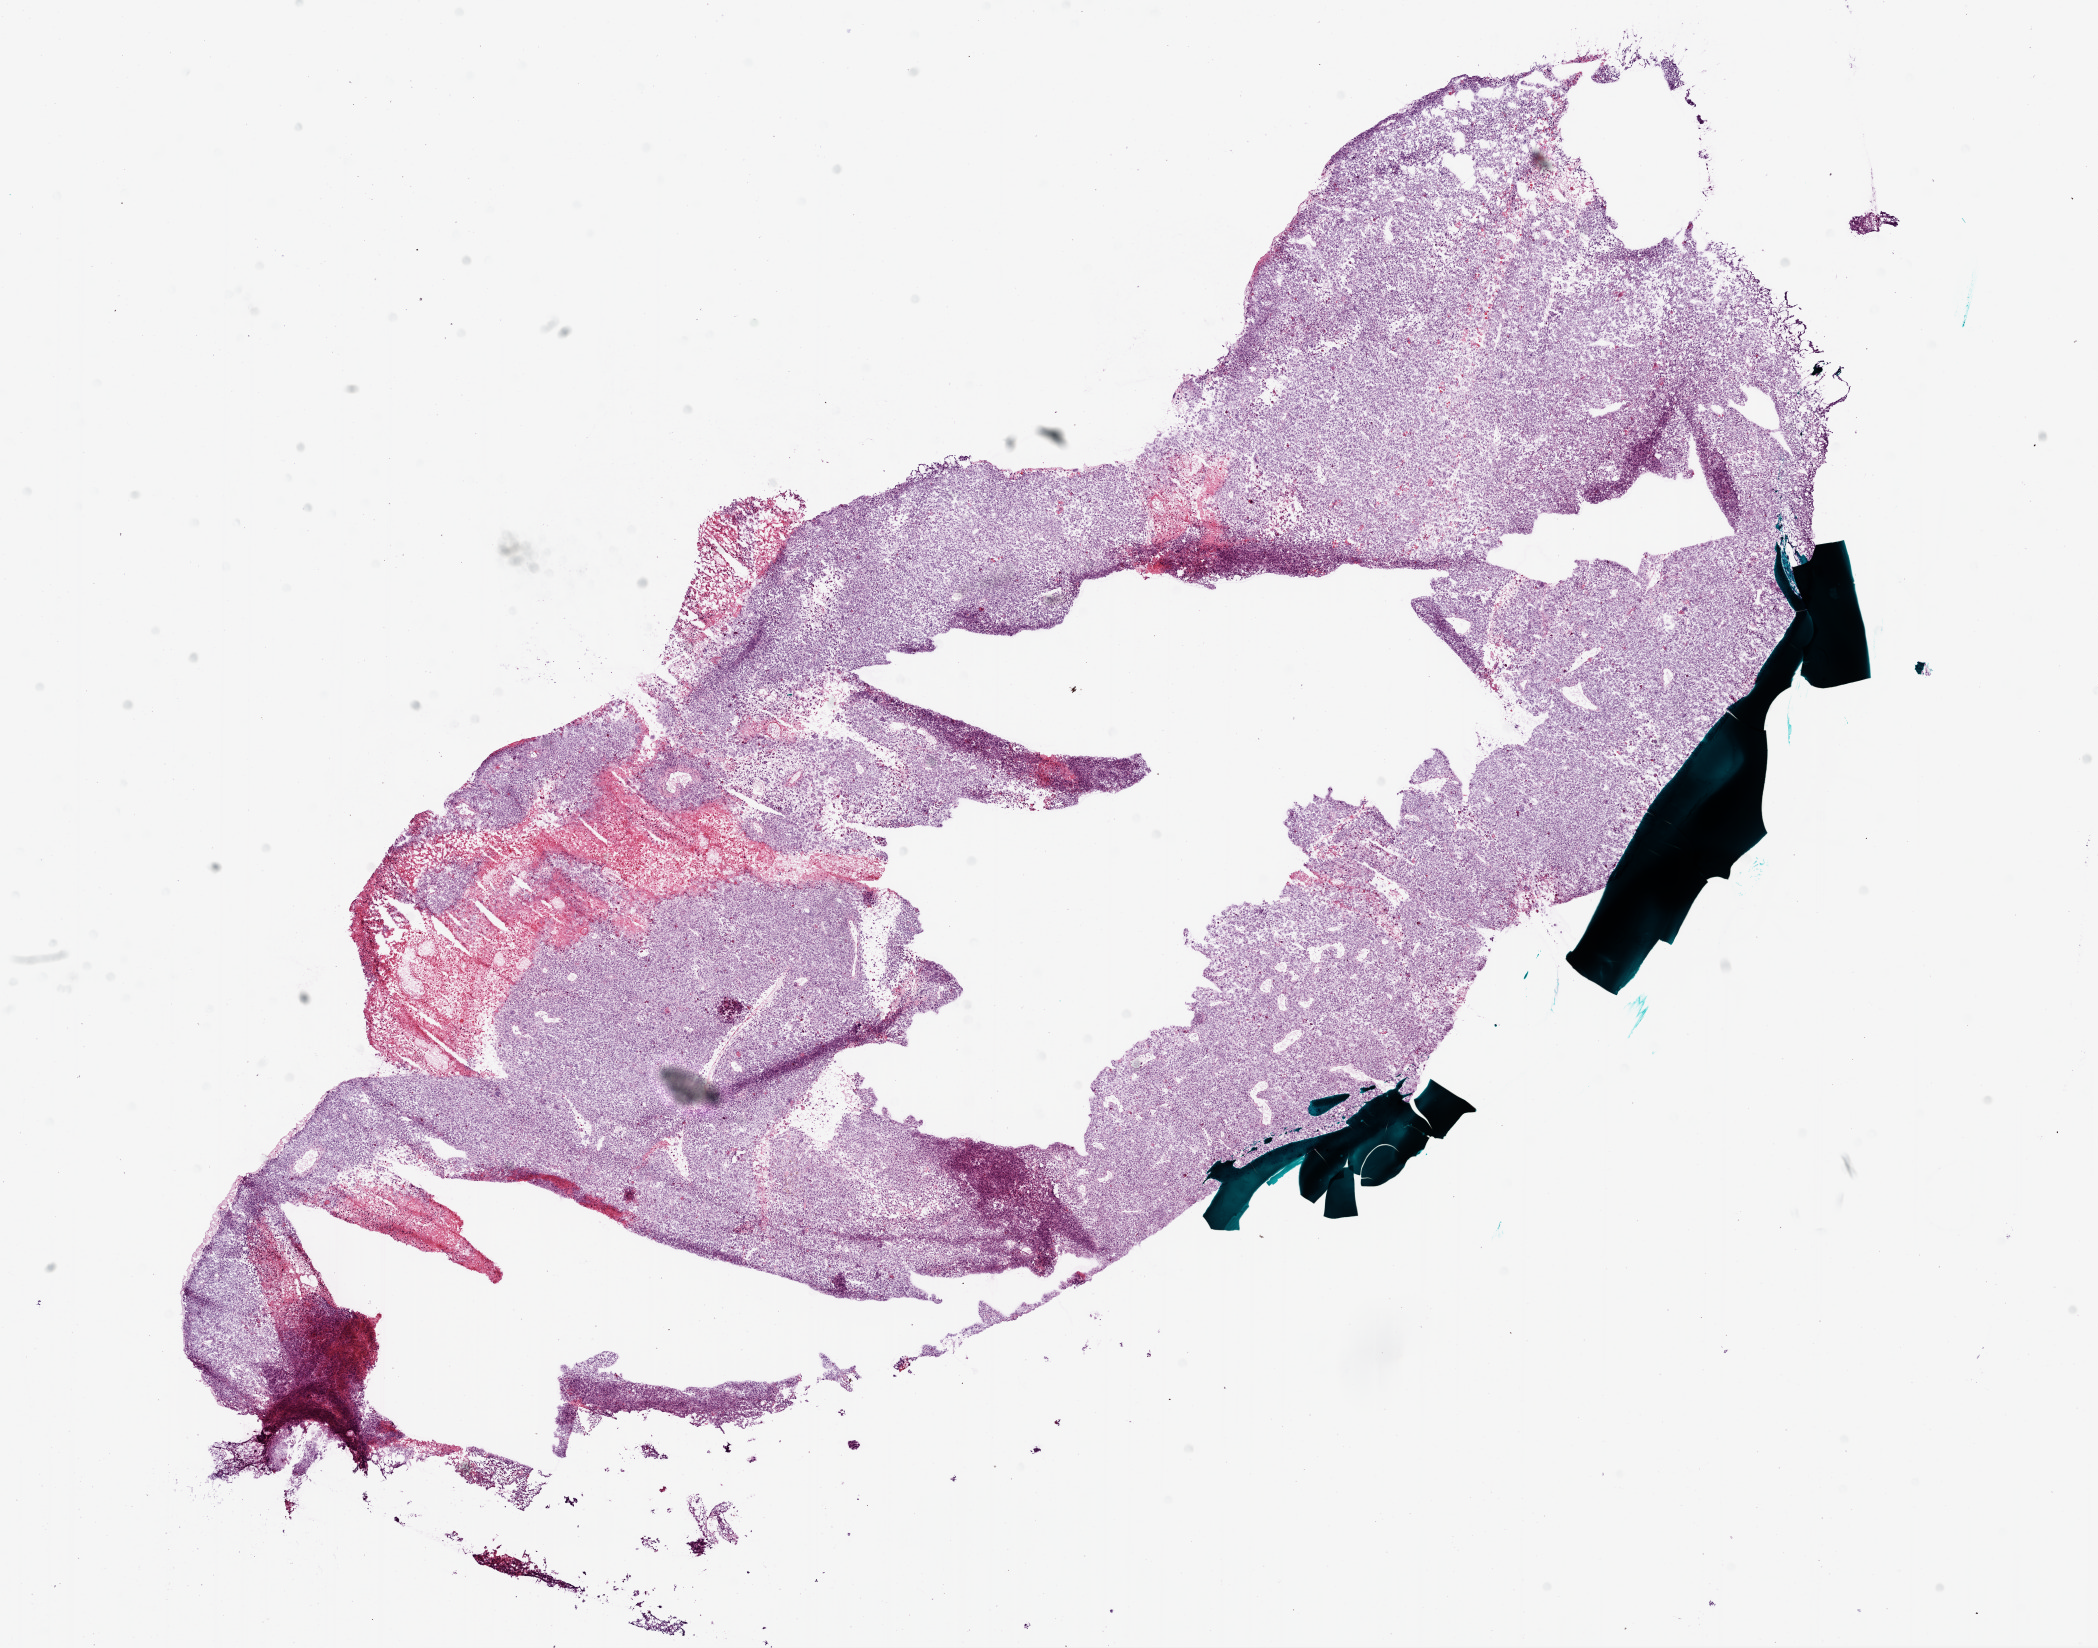
Digitized Hematoxylin and eosin (H&E) stained tissue section (whole slide), shown as a low-resolution overview of the whole scanned area (about 16.9 x 13.3 mm). Frozen section from the bottom of the tissue portion. Primary tumour sample from the brain. Female patient; age at initial diagnosis 74 years. Slide review estimates, as recorded: tumour cells 90%, tumour nuclei 100%, normal cells 0%, stromal cells 0%, necrosis 10%.
• histologic diagnosis: Glioblastoma